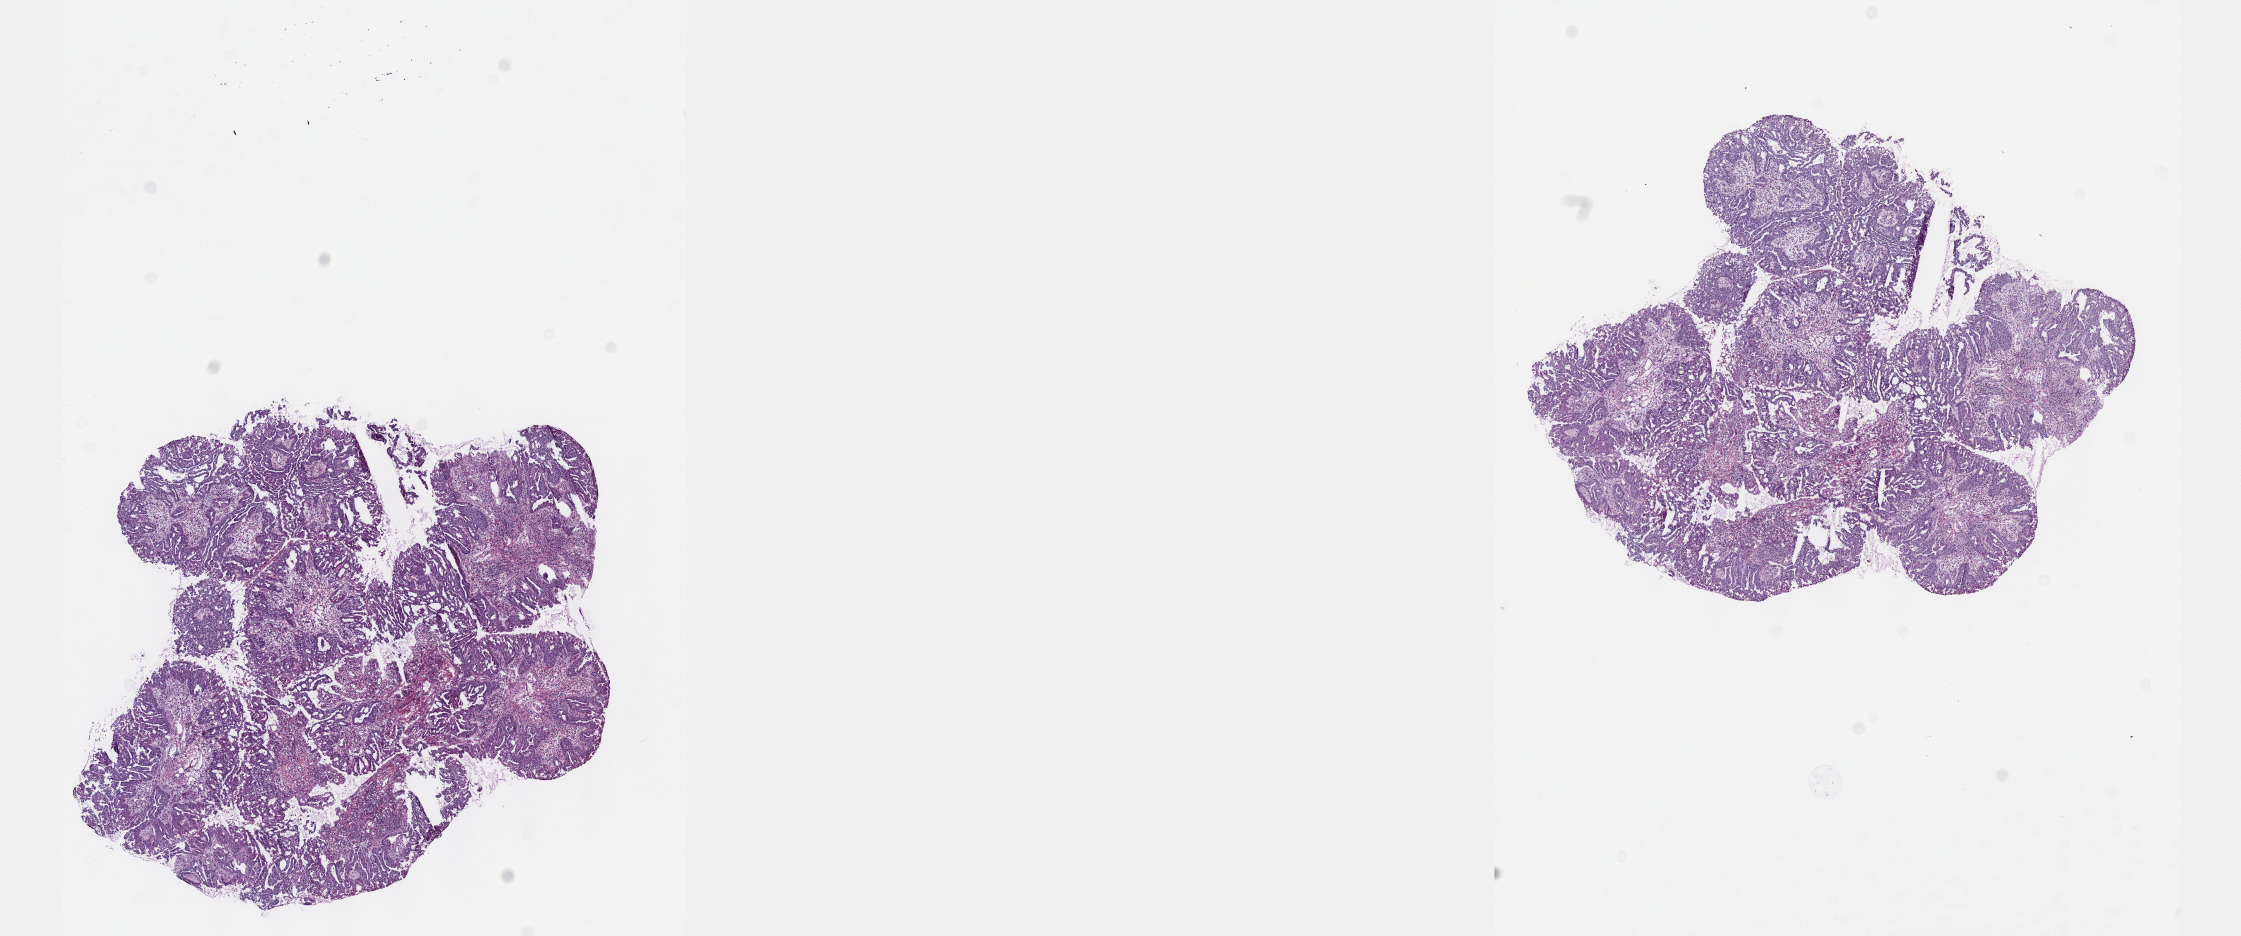
H&E-stained whole-slide image, shown as a low-resolution overview of the whole scanned area (about 18.1 x 7.6 mm, slide scanned at 40x). Frozen section. Cervix, primary tumour sample. Patient: female, age at initial diagnosis 53 years.
Diagnosis: Mucinous adenocarcinoma, endocervical type (cervix uteri).